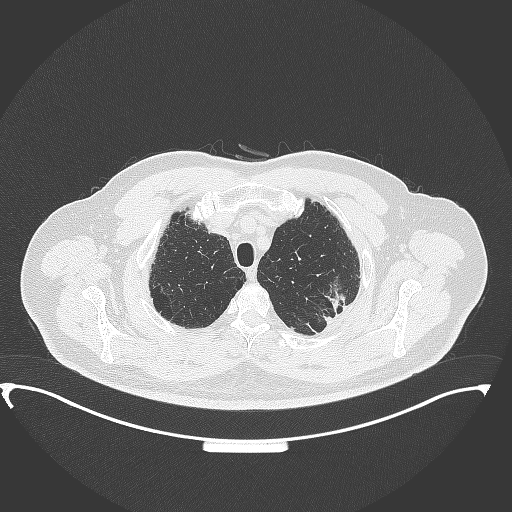
Chest CT, one axial slice; slice 310 of 350 in the series (ordered by position); lung window (W 1500 / L -600 HU); 1 mm slice thickness; 512 × 512 image matrix, field of view 459 × 459 mm. Patient: male, 64 years. From the clinical record (not read from this slice): clinical TNM (as recorded): T1c N1 M1.
Structures marked on this image (bounding box drawn by a radiologist):
- lung tumour (recorded histology: adenocarcinoma): box from (x=319, y=268) to (x=351, y=315) px